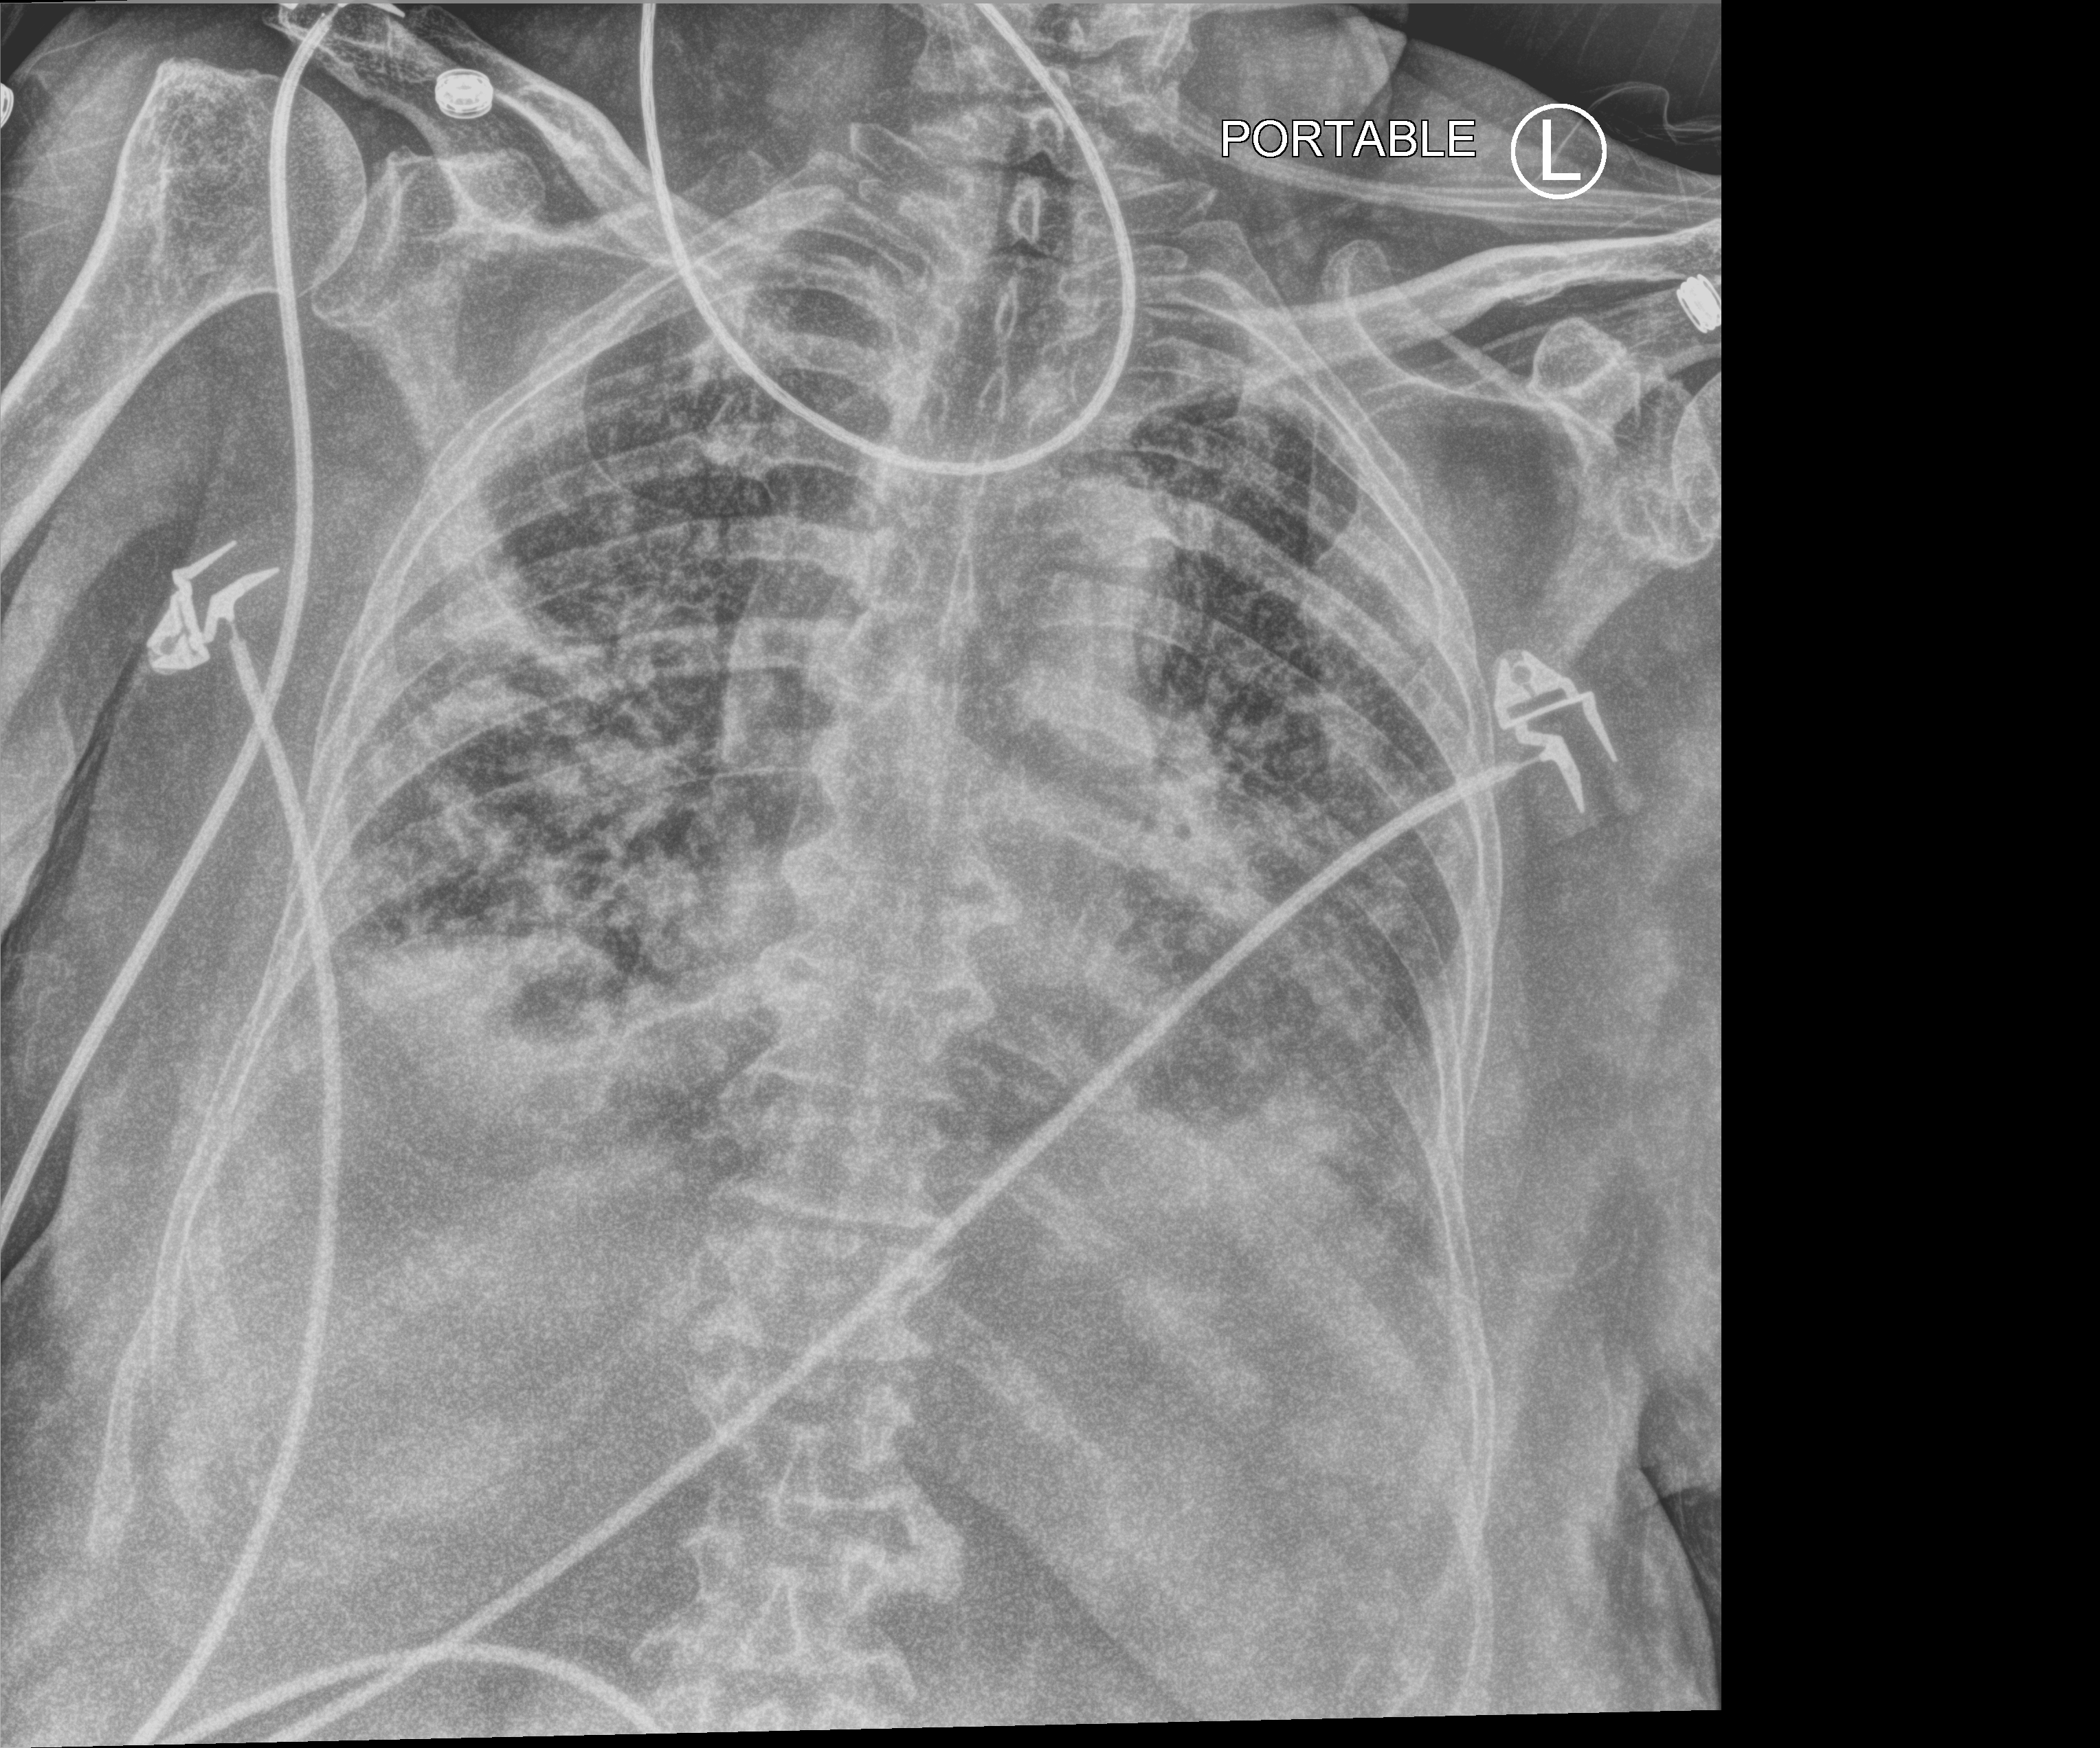
Bedside chest radiograph (computed radiography), anteroposterior (AP) projection. Female patient hospitalised with COVID-19, age 75–90 years.
From the hospital-stay record, not from the radiograph (when in the stay this image was taken is not recorded): admitted to intensive care during this hospital stay: yes.